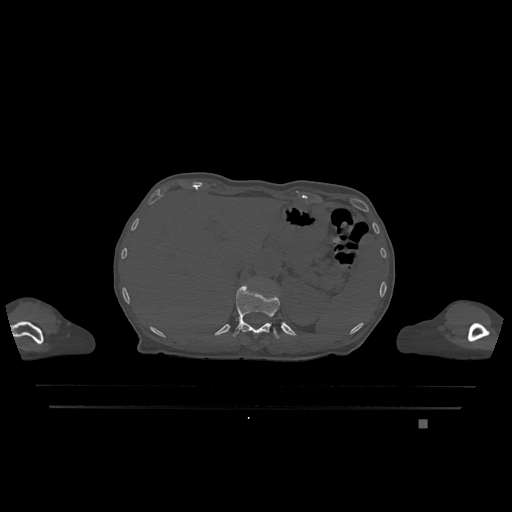
CT including the spine, one axial slice; position 530 of 1317 along the scan axis; bone window (W 1800 / L 400 HU); 0.5 mm slice thickness; 512 × 512 image matrix, field of view 500 × 500 mm. Patient: female, 74 years. Case-level facts recorded for this patient, not image findings: primary cancer: lung.
Annotated regions visible in this slice (semi-automatic segmentation, software-assisted and operator-edited):
- T12 vertebra: bounding box <233,283,280,339> (left, top, right, bottom; pixels)